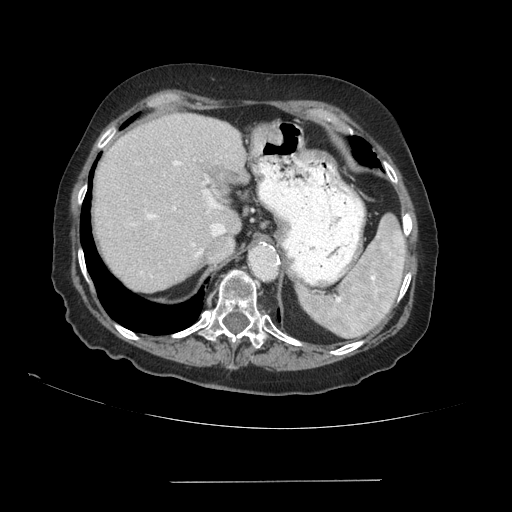
Contrast-enhanced abdominal CT (liver protocol), one axial slice. Position 67 of 89 along the scan axis. 140 kVp. Soft-tissue window (W 400 / L 40 HU). 2.5 mm slice thickness. 512 × 512 image matrix, field of view 400 × 400 mm. From the clinical record (not read from this slice): diagnosis: hepatocellular carcinoma (patient treated with transarterial chemoembolisation; whether this scan precedes or follows treatment is not stated here); TNM stage (as recorded): Stage-IVA; Child-Pugh class: A; tumour nodularity: uninodular.
Outlined on this slice (semi-automatic segmentation, software-assisted and operator-edited):
- abdominal aorta: box from (x=251, y=246) to (x=275, y=278) px
- liver parenchyma outside the tumour (the mass and vessels are separate outlines, so this box may not span the whole liver): (x=92, y=114)–(x=246, y=292)
- liver vessels: (x=147, y=161)–(x=226, y=256)